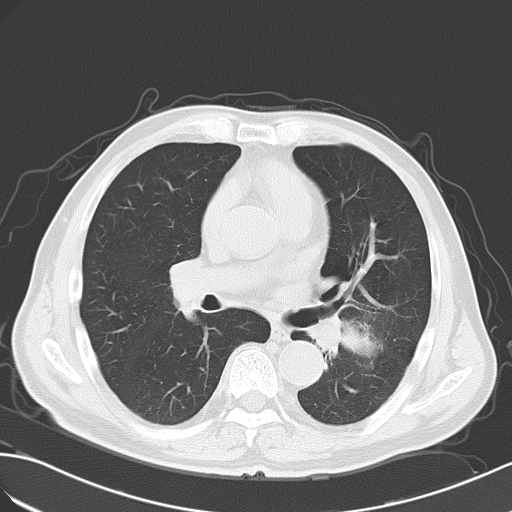
Chest CT, one axial slice. Slice 30 of 55 in the series (ordered by position). Reconstruction kernel B70f. 120 kVp. Lung window (W 1500 / L -600 HU). 5 mm slice thickness. 512 × 512 image matrix, field of view 353 × 353 mm. Male patient, age 63 years. Case-level facts recorded for this patient, not image findings: clinical TNM (as recorded): T3 N3 M1a; histopathological grade: G3.
Outlined on this slice (bounding box drawn by a radiologist):
- lung tumour (recorded histology: large cell carcinoma): bounding box <343,315,379,372> (left, top, right, bottom; pixels)